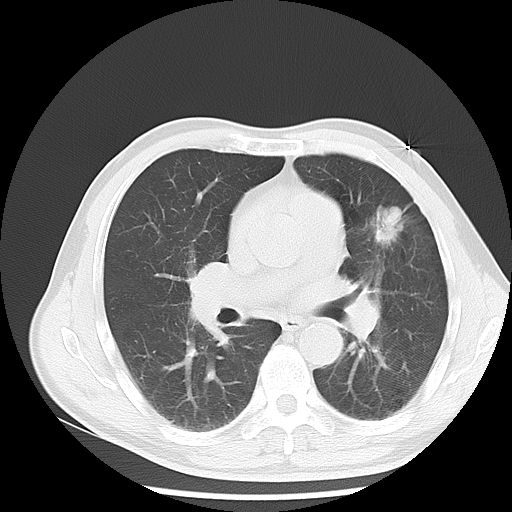
Chest CT, one axial slice. Slice 9 of 13 in the series (ordered by position). Lung window (W 1500 / L -600 HU). 5 mm slice thickness. 512 × 512 image matrix, field of view 350 × 350 mm. Patient: male, 54 years. From the clinical record (not read from this slice): clinical TNM (as recorded): T1c N0 M0.
Annotated regions visible in this slice (rectangle marked by the reading radiologist):
- lung tumour (recorded histology: adenocarcinoma): bounding box <369,198,408,250> (left, top, right, bottom; pixels)